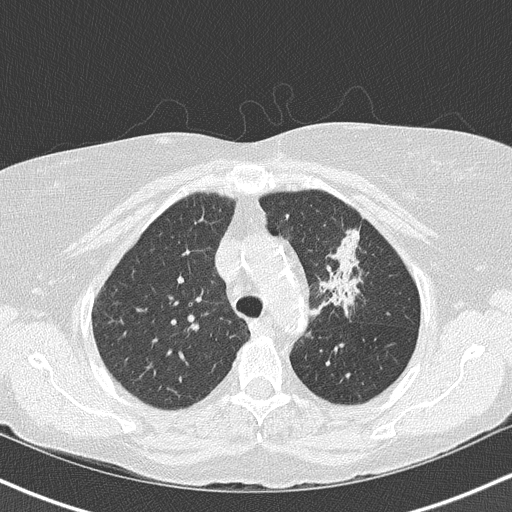
Chest CT (low-dose screening protocol), one axial image, third screening round (two years after baseline), lung window (W 1500 / L -600 HU), 2 mm slice thickness. Female, age 68 years at enrolment. Former smoker at enrolment.
Expert reader's lesion annotation, bounding box <299,213,382,321> (left, top, right, bottom; pixels). Reader record for this screening exam (exam-level; its link to the box is not recorded): non-calcified nodule or mass ≥4 mm, left upper lobe, 5 × 5 mm, poorly defined margins, mixed attenuation, pre-existing on the prior screen: yes; interval growth: yes. Participant outcome: lung cancer diagnosed 42 days after this screen — adenocarcinoma, NOS, left upper lobe, poorly differentiated (G3), stage IB (AJCC 6th edition), 50 mm at pathology.